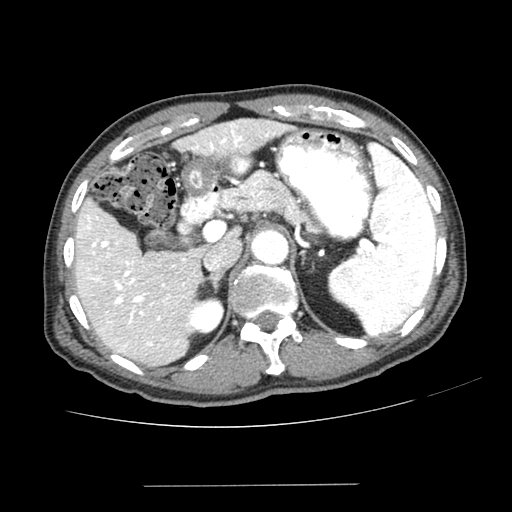
Contrast-enhanced abdominal CT (liver protocol), one axial slice; slice 153 of 187 in the series (ordered by position); reconstruction kernel SOFT; 100 kVp; one of 2 acquisitions stored at this slice position; soft-tissue window (W 400 / L 40 HU); 512 × 512 image matrix, field of view 360 × 360 mm. From the clinical record (not read from this slice): diagnosis: hepatocellular carcinoma (patient treated with transarterial chemoembolisation; whether this scan precedes or follows treatment is not stated here); TNM stage (as recorded): Stage-I.
Annotated regions visible in this slice (semi-automatically segmented with operator editing):
- liver parenchyma outside the tumour (the mass and vessels are separate outlines, so this box may not span the whole liver): bounding box (x1, y1, x2, y2) in pixels: (74, 118, 286, 366)
- liver vessels: (80, 123, 269, 348)